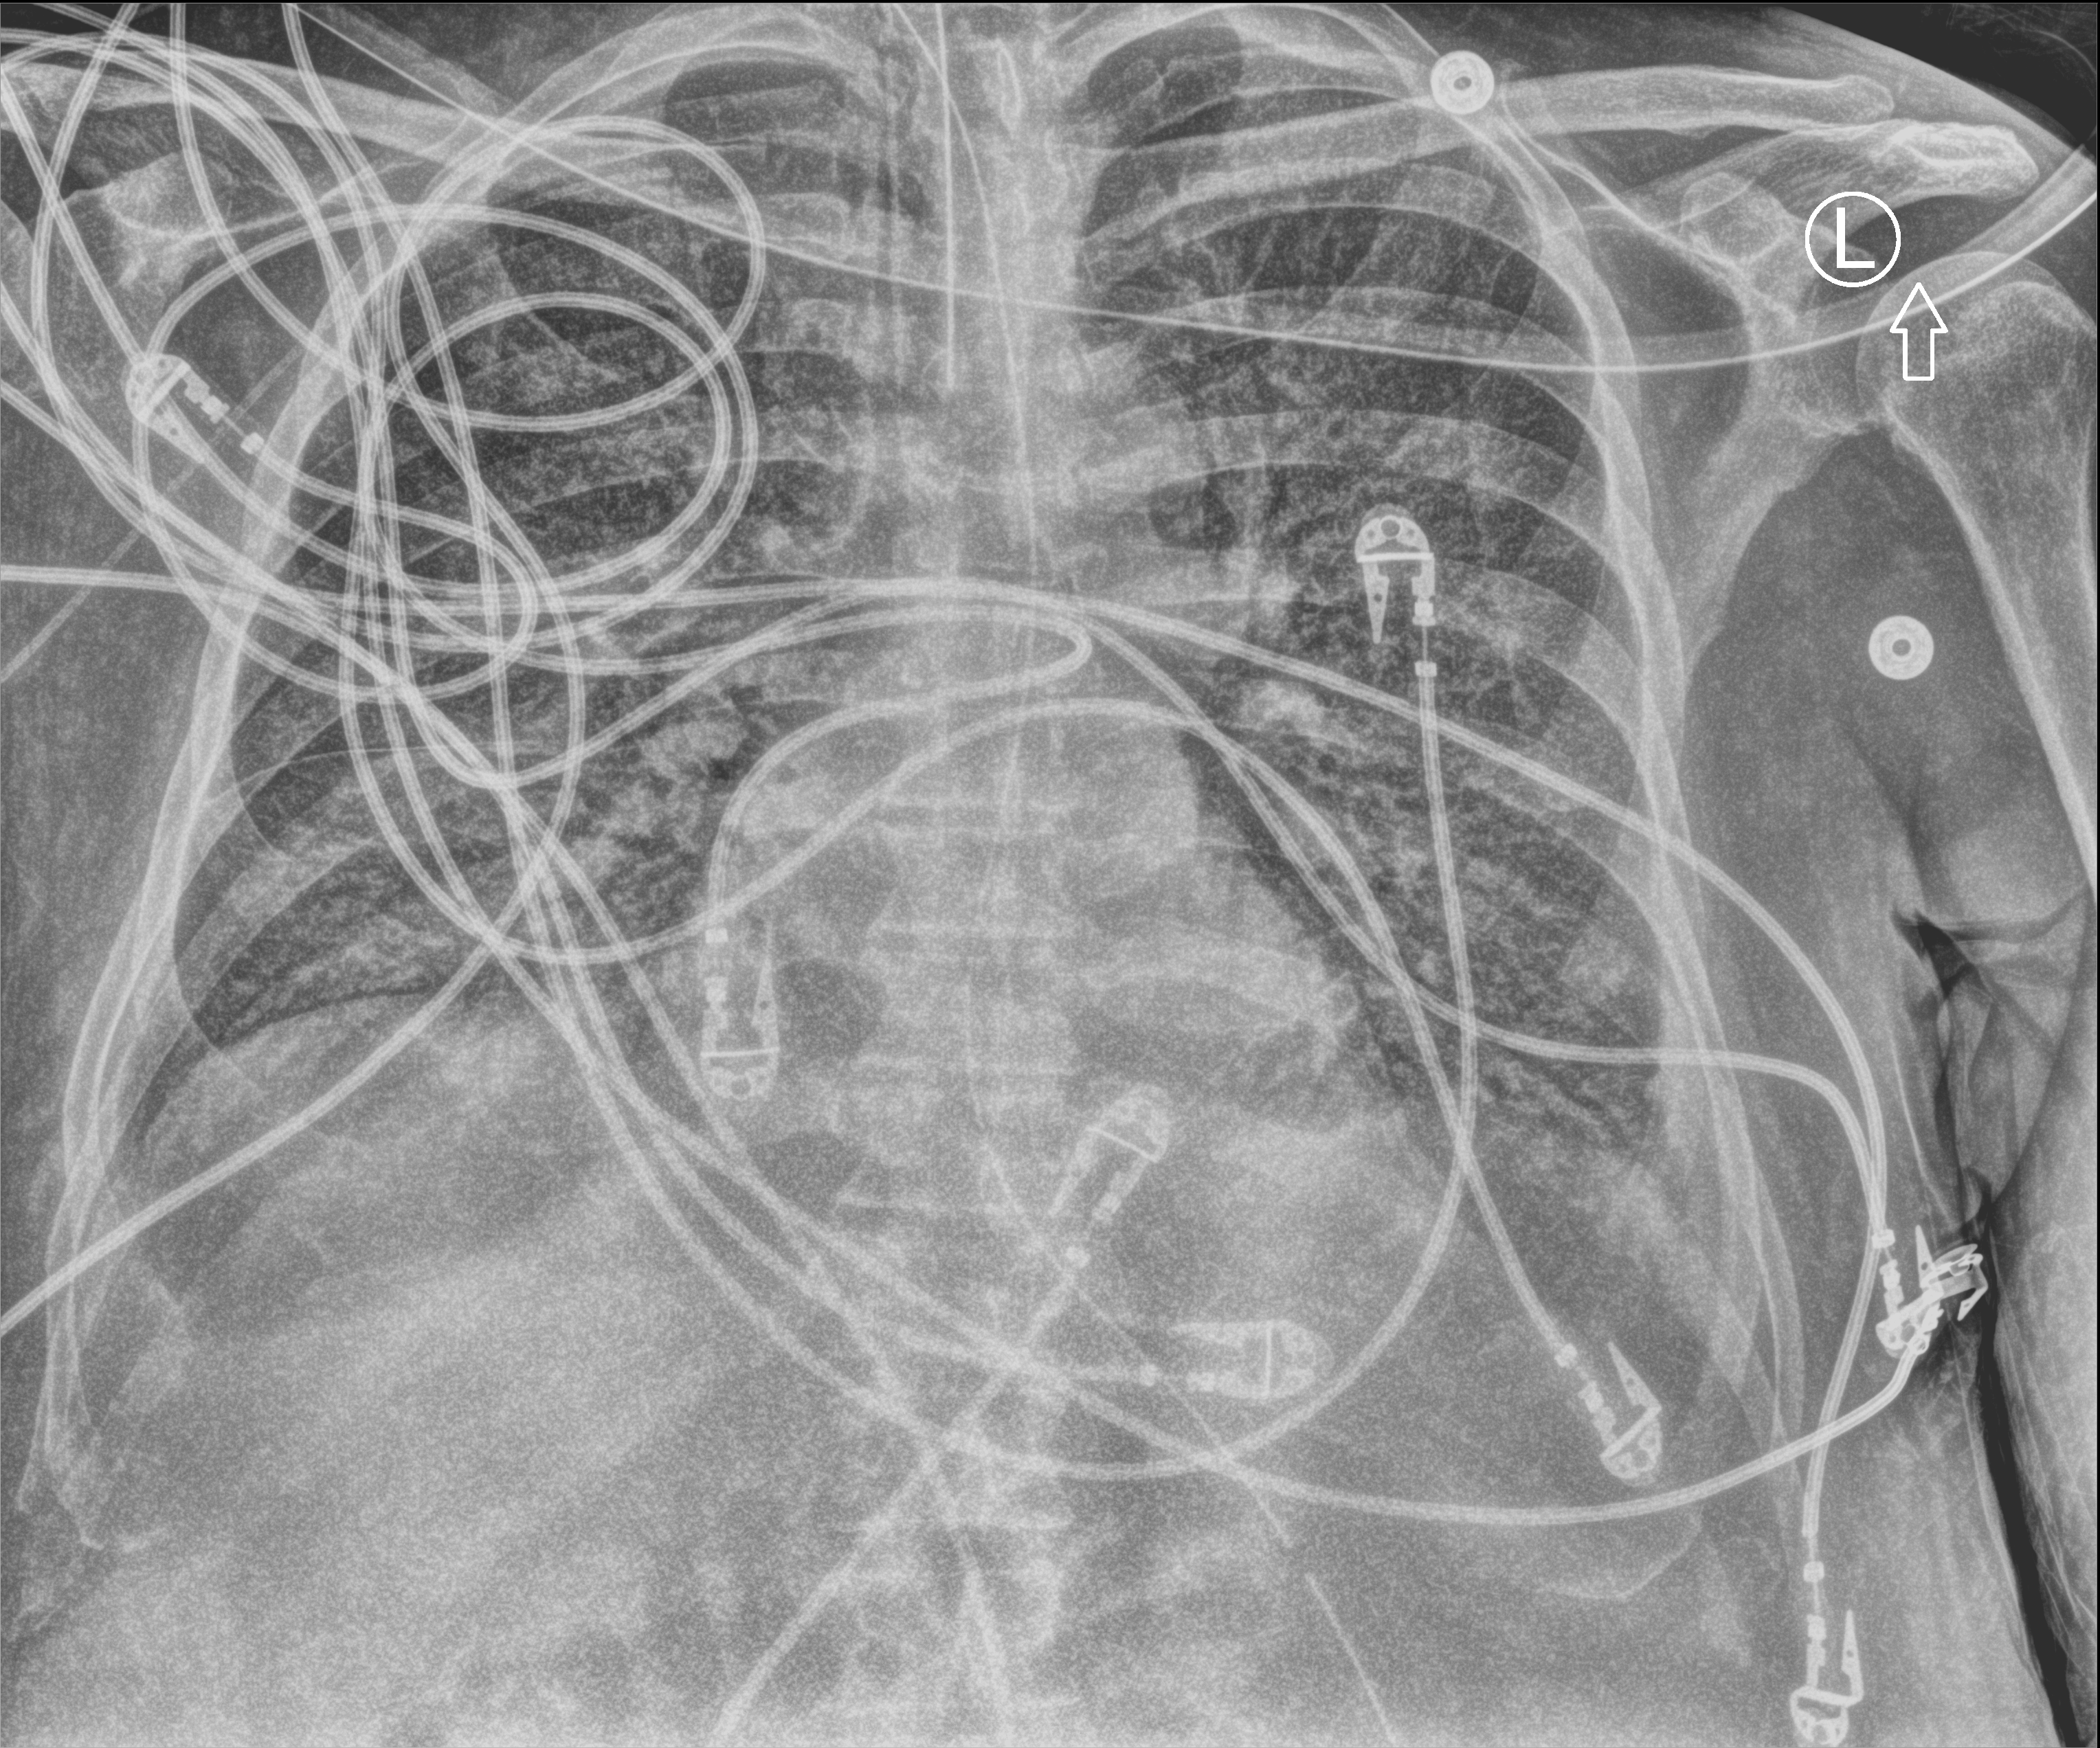
Chest X-ray (portable); anteroposterior (AP) projection. Patient hospitalised with COVID-19; male, aged 60–74 years.
Hospital-stay facts (about this admission, not read from this image; timing relative to this image not recorded): mechanically ventilated during this hospital stay: yes.